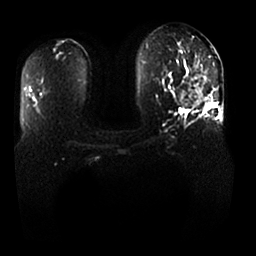
Breast MRI, one axial slice; slice 13 of 25 in the series (ordered by position); diffusion-weighted series; image 2 of 4 stored at this slice position (different b-values; order by instance number); 1.5 T; 4 mm slice thickness; 256 × 256 image matrix. Female patient.
Outlined on this slice (expert manual segmentation):
- tumour on diffusion-weighted imaging: box from (x=179, y=64) to (x=201, y=108) px